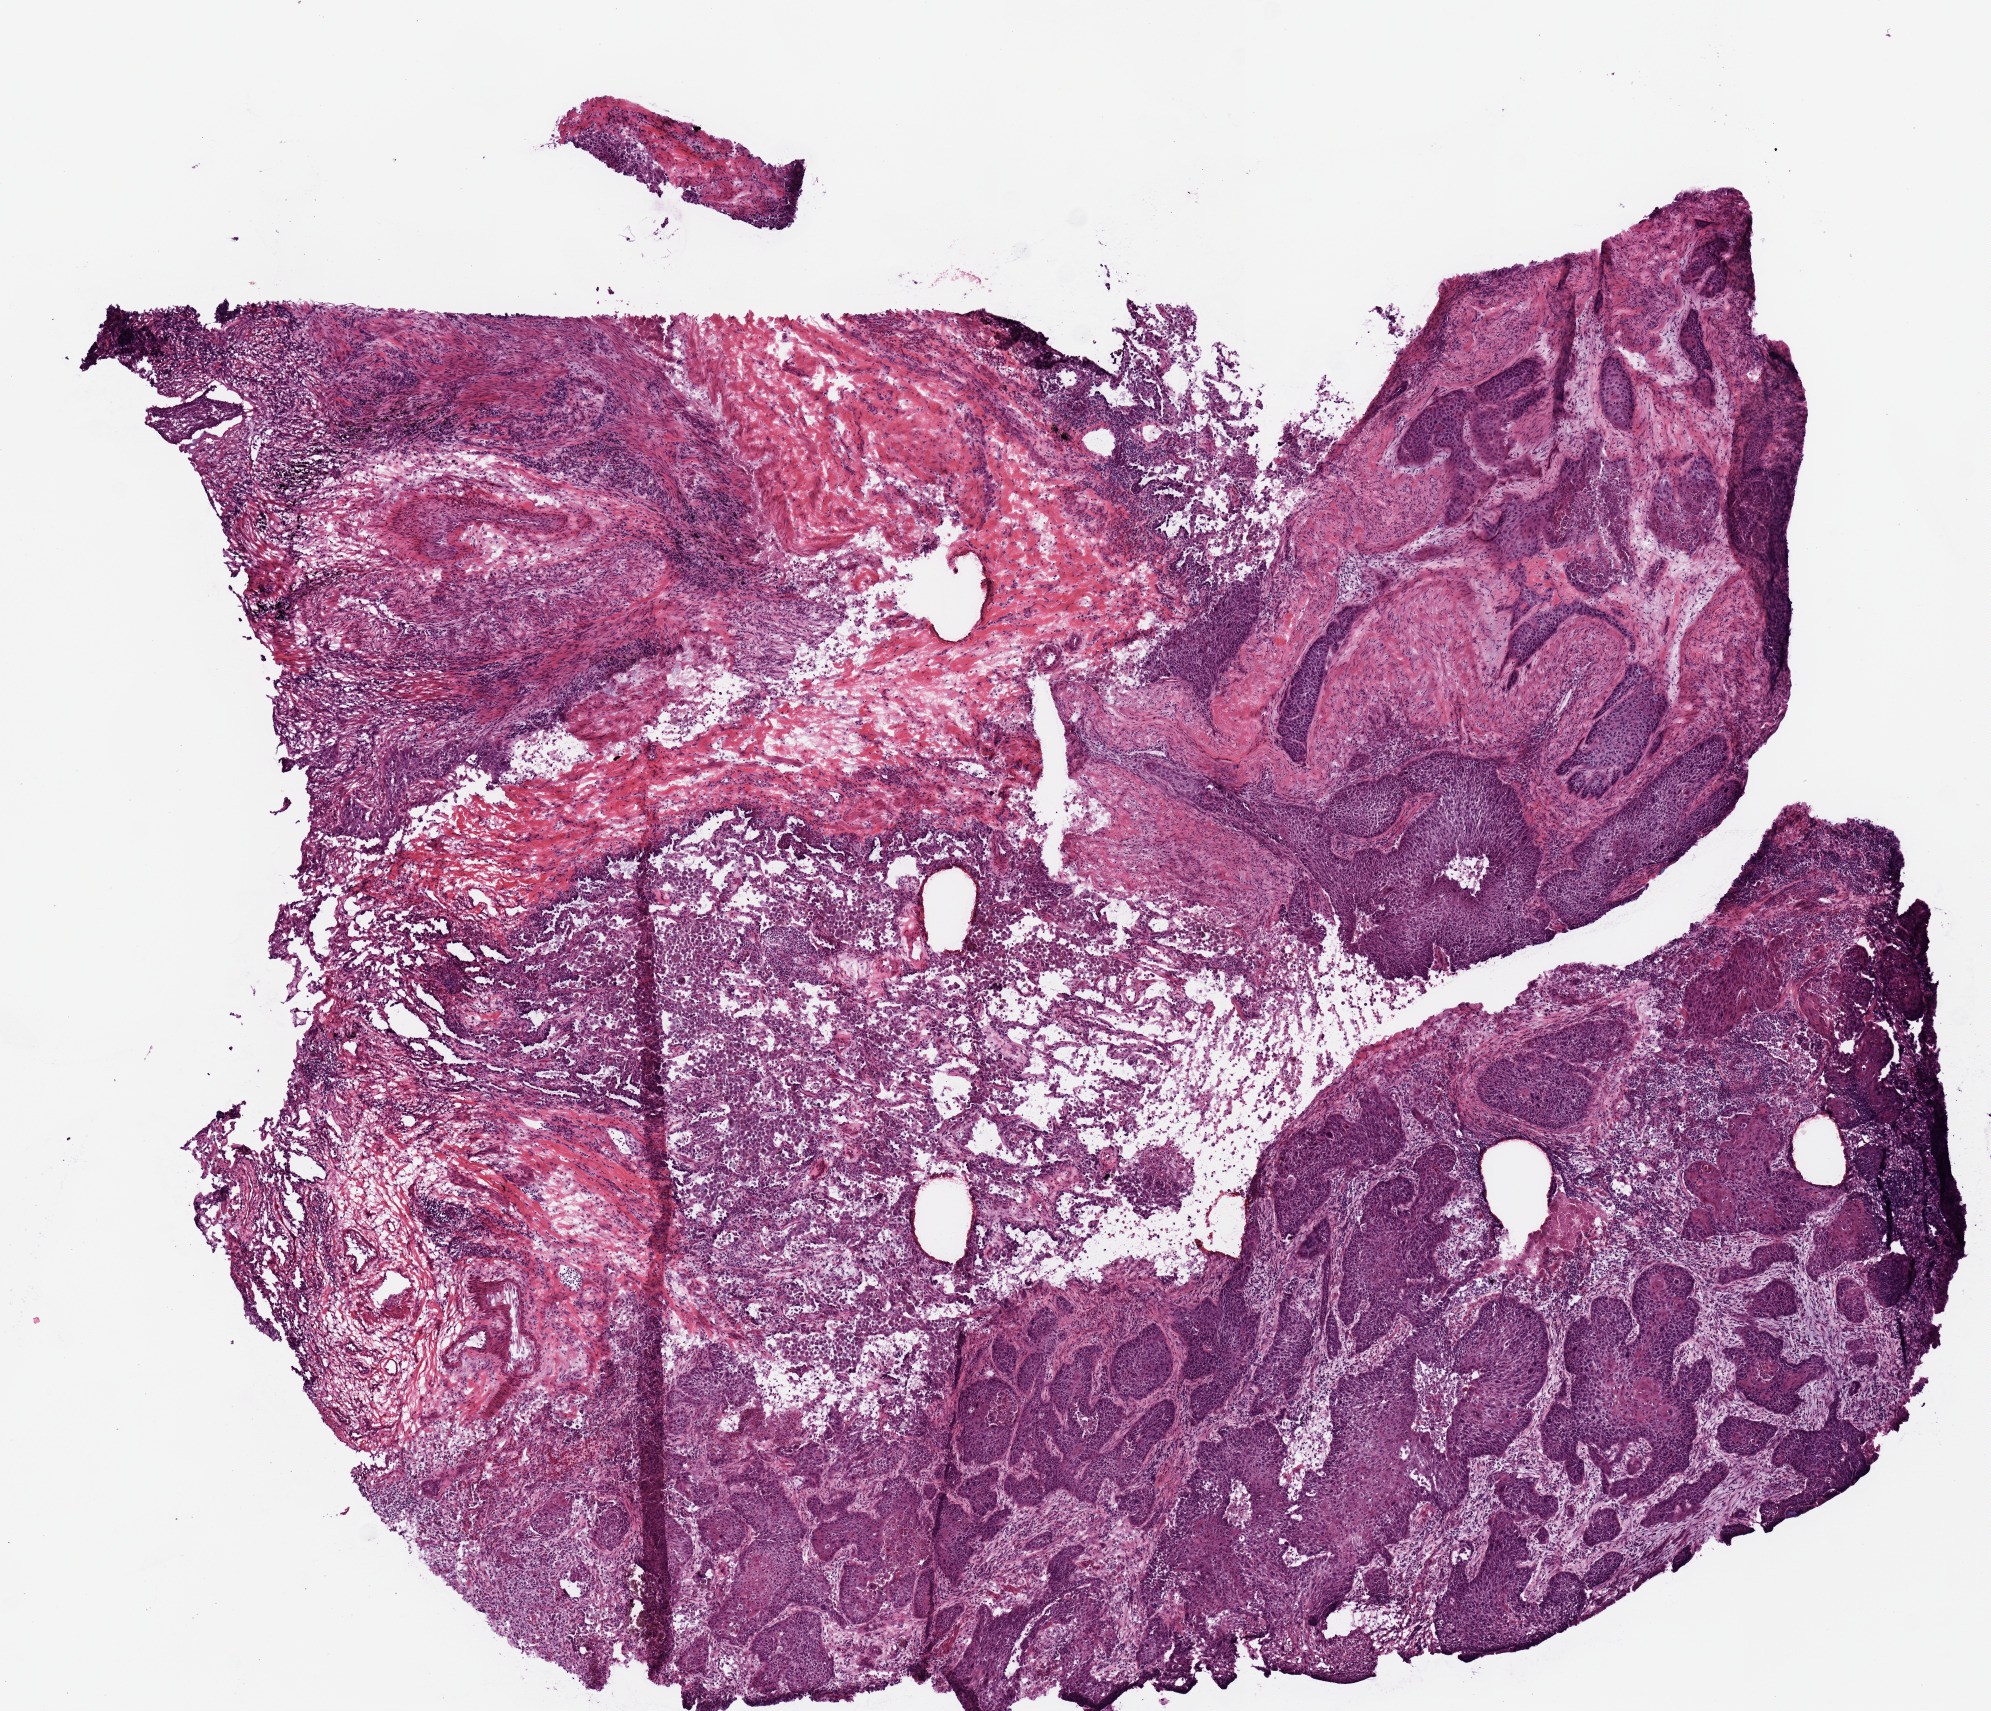
Digitized H&E-stained tissue section (whole slide), low-resolution overview of the scanned area, about 7.9 x 6.8 mm (from a 20x scan), frozen section from the top of the tissue portion, primary tumour sample from the lung. Male patient; age at initial diagnosis 55 years. Slide review estimates, as recorded: tumour cells 75%, tumour nuclei 65%, normal cells 0%, stromal cells 25%, necrosis 0%. Infiltration values recorded for this section: lymphocyte infiltration 0%, monocyte infiltration 0%, neutrophil infiltration 0%.
* diagnosis: Squamous cell carcinoma, NOS (upper lobe, lung)
* AJCC pathologic stage: IIA